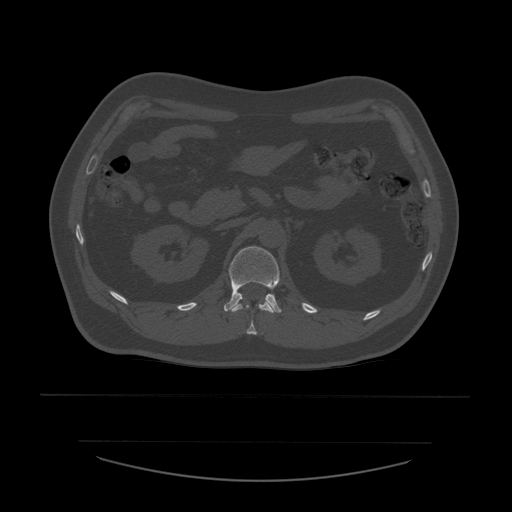
CT including the spine, one axial slice; reconstruction kernel STANDARD; 120 kVp; bone window (W 1800 / L 400 HU); 1.25 mm slice thickness; 512 × 512 image matrix, field of view 441 × 441 mm. Patient age 44 years. From the clinical record (not read from this slice): primary cancer: soft tissue sarcoma.
Outlined on this slice (semi-automatically segmented with operator editing):
- L1 vertebra: bounding box (x1, y1, x2, y2) in pixels: (224, 246, 282, 313)
- T12 vertebra: (232, 301, 274, 335)